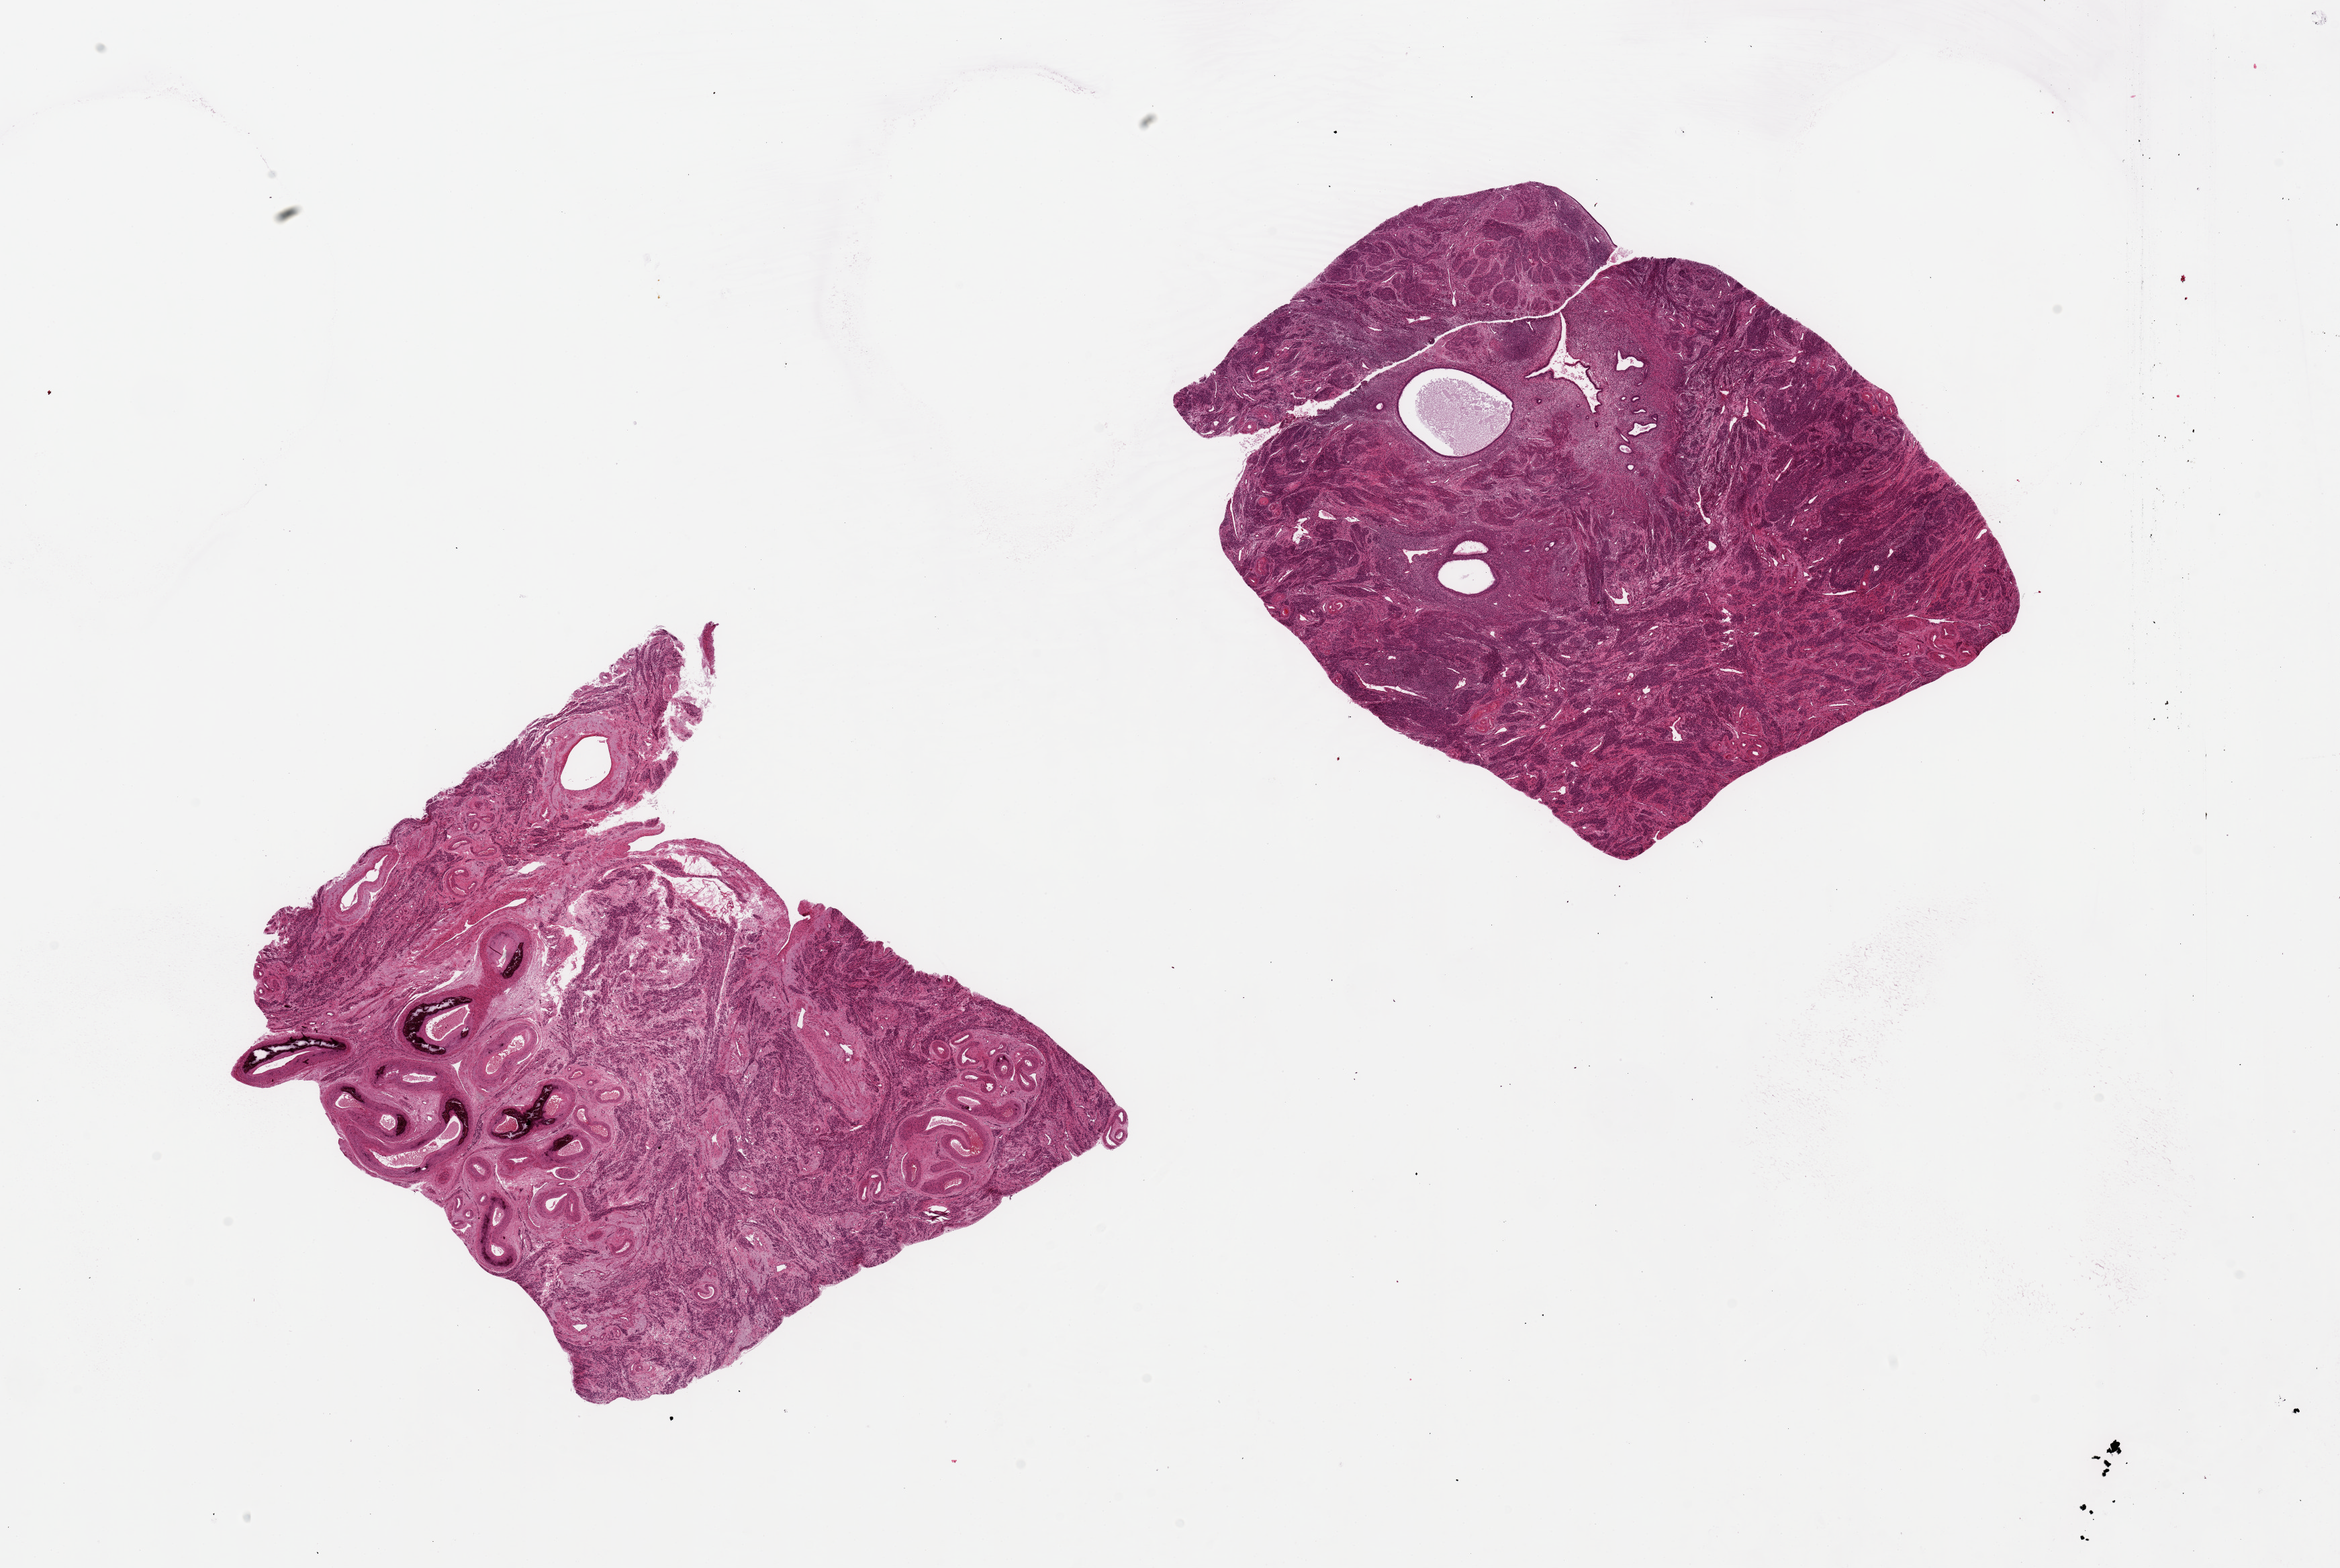
H&E whole-slide image, whole scanned area (about 27.6 x 18.5 mm, from a 20x scan) shown as a low-resolution overview; PAXgene-fixed paraffin-embedded (PFPE) section; sampled site (target tissue): uterus; tissue donor sample. Donor: female.
Reviewer comment on this tissue sample: 2 pieces, 8x8 & 8x7mm; 1 has 3 areas of endometrium cut obliquely; other is only myometrium in this section.